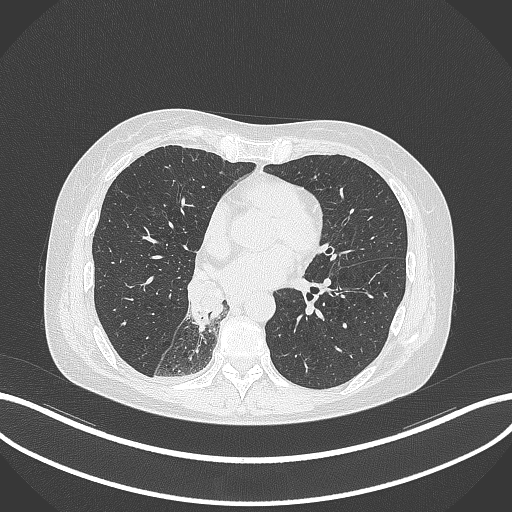
Chest CT, one axial slice; slice 136 of 329 in the series (ordered by position); reconstruction kernel B70f; lung window (W 1500 / L -600 HU); 1 mm slice thickness; 512 × 512 image matrix, field of view 400 × 400 mm. Female patient, age 63 years. Case-level facts recorded for this patient, not image findings: clinical TNM (as recorded): T1c N0 M0.
Structures marked on this image (rectangle marked by the reading radiologist):
- lung tumour (recorded histology: adenocarcinoma): bounding box <183,268,226,328> (left, top, right, bottom; pixels)